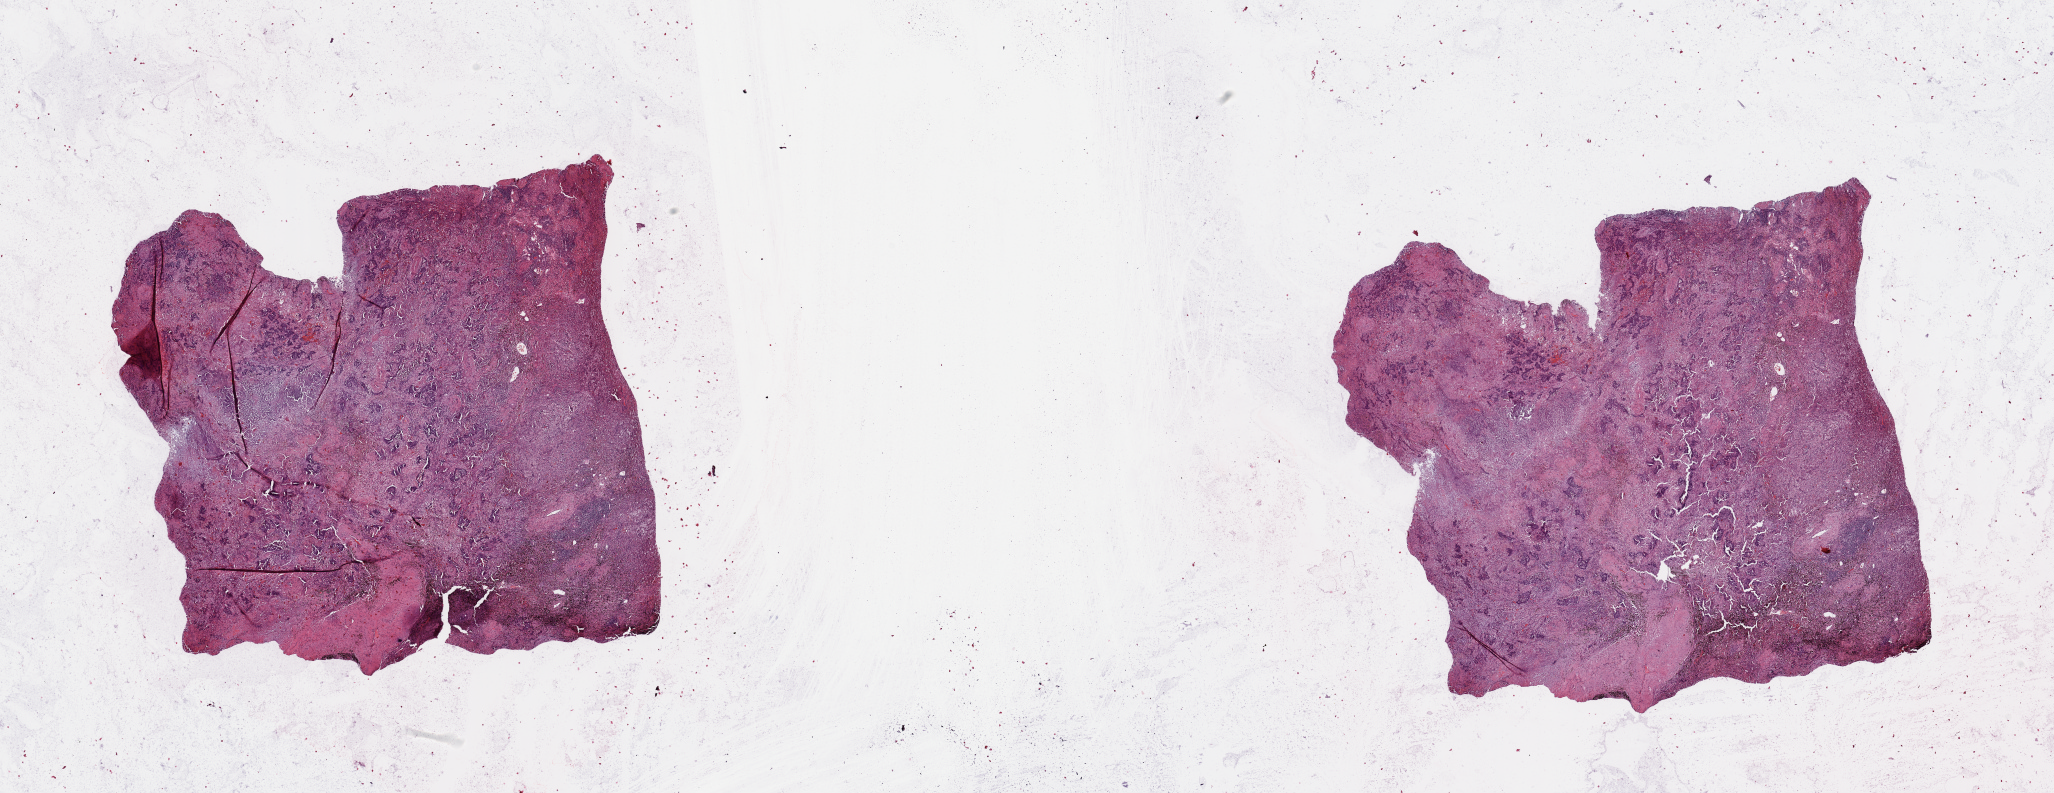
H&E whole-slide image — low-resolution overview of the scanned area, about 32.5 x 12.5 mm, lung, tumour tissue. 72-year-old male patient. Histologic grade: G3 (poorly differentiated).
- histologic diagnosis: Squamous cell carcinoma, NOS
- AJCC pathologic stage: IIIA